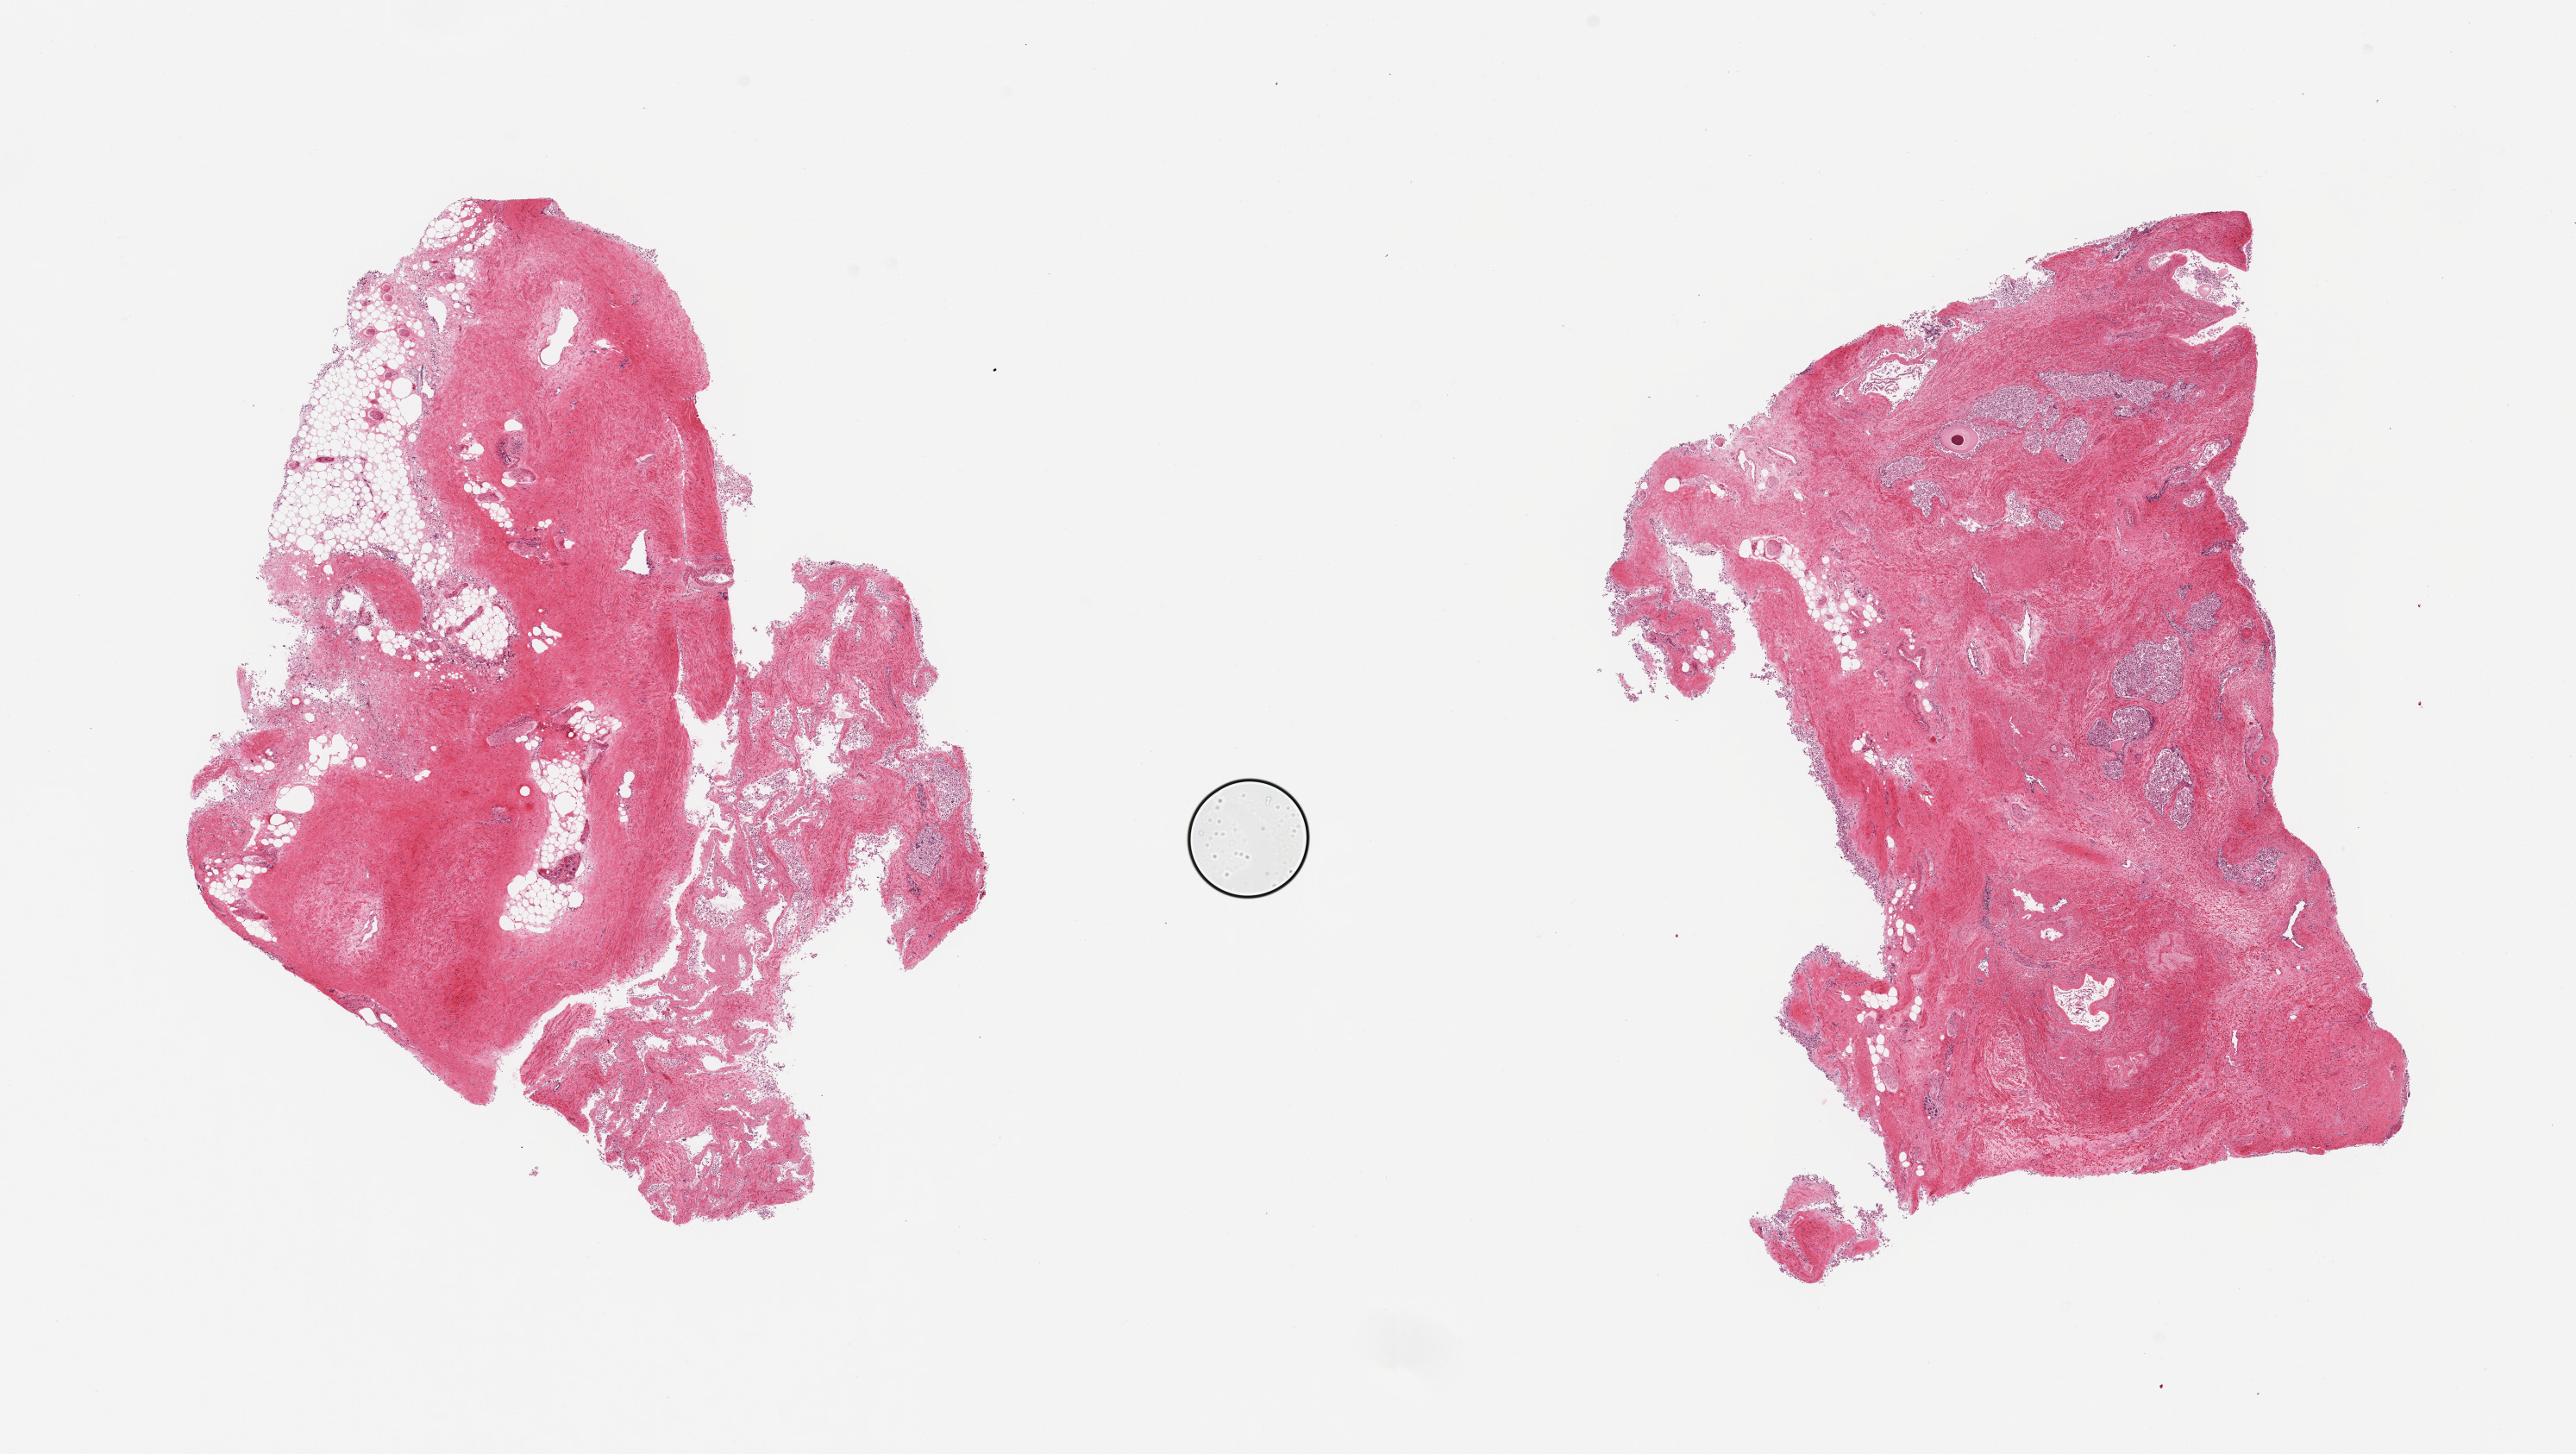
Whole-slide image, hematoxylin and eosin (H&E) stain — whole scanned area (about 23.6 x 13.3 mm) shown as a low-resolution overview. PAXgene-fixed, paraffin-embedded tissue. Sampled site (target tissue): prostate. Donor tissue sample. Donor sex: male.
- pathologist's review note for this sample: 2 pieces; fibromuscular stroma with nerves and ganglions and prostatic glands with widely sloughed epithelium; one piece with attached ~15%external fat